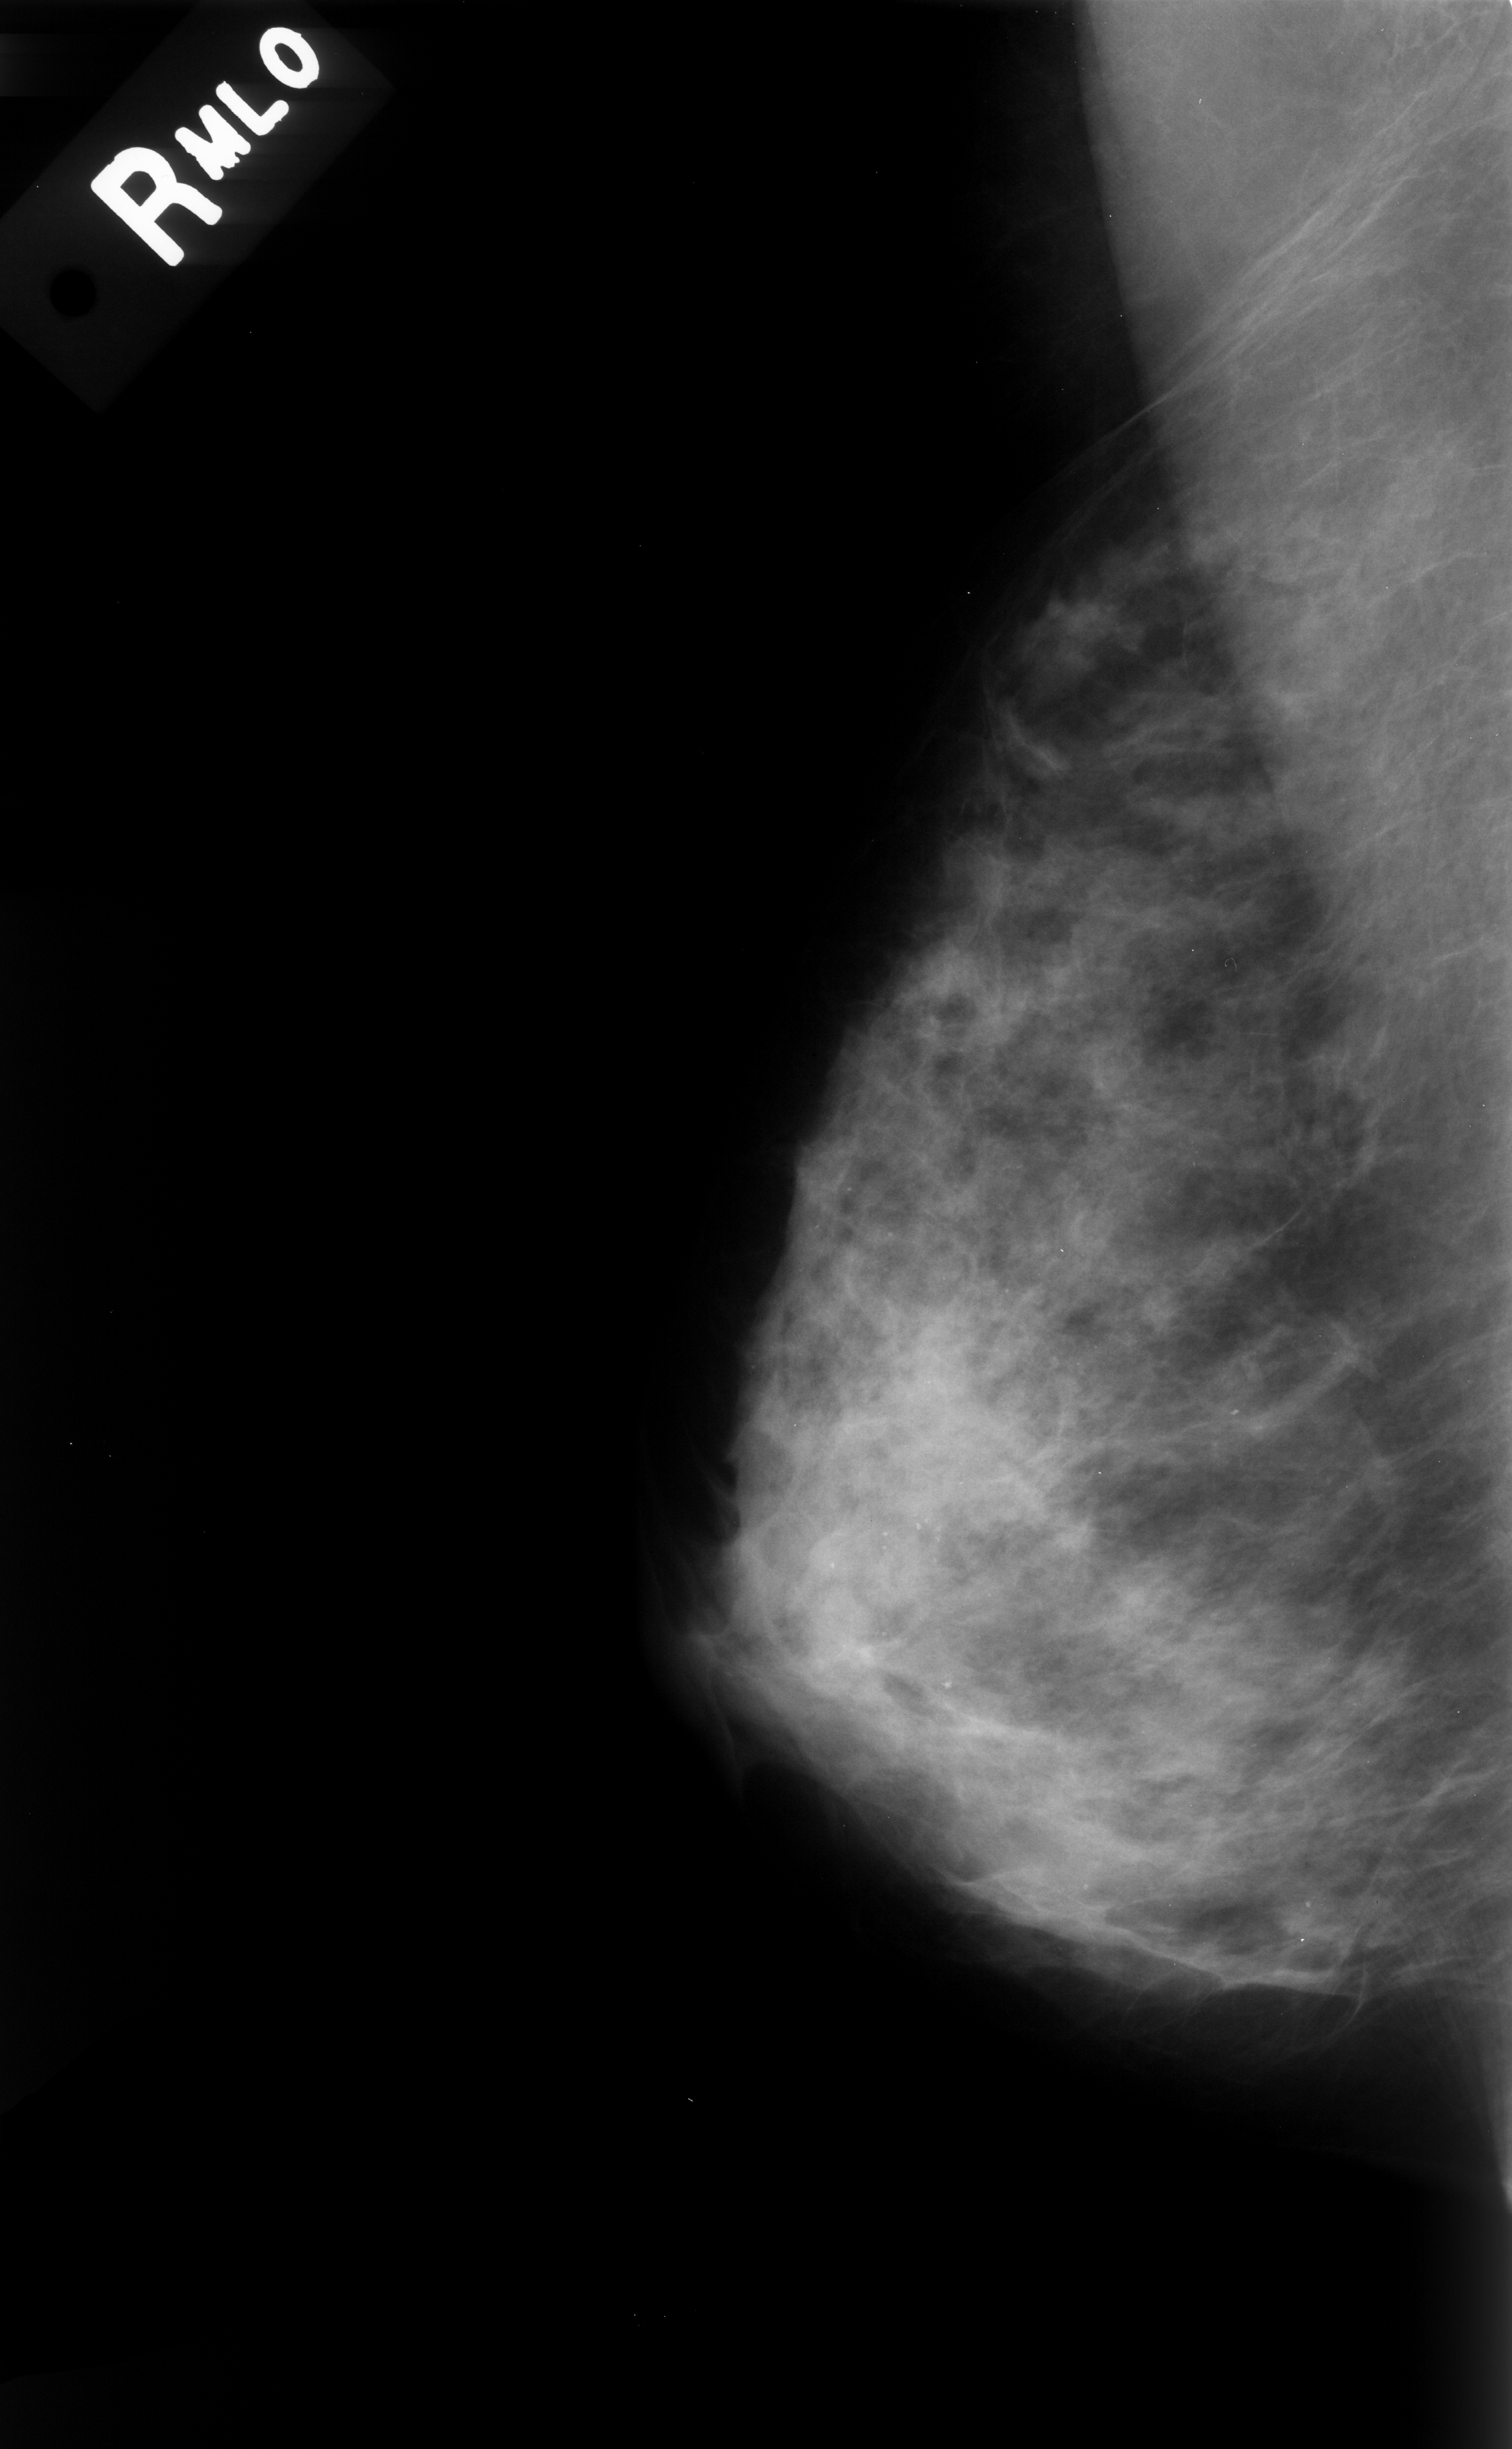
Scanned film-screen mammogram, right breast, MLO view, BI-RADS breast density category 3 (scale 1–4).
Abnormality record for this image: calcifications, morphology pleomorphic, distribution diffusely scattered; BI-RADS assessment category 3; subtlety rating 3 on a 1 (subtle) to 5 (obvious) scale; pathology result (as recorded, not read from the image): benign.